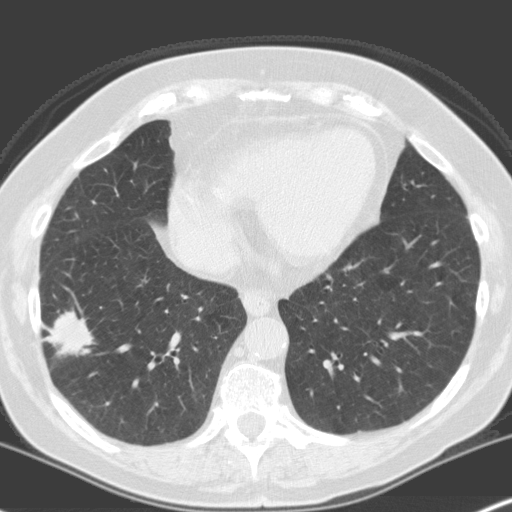
Low-dose screening chest CT, one axial slice. Position 64 of 160 along the scan axis. 120 kVp. Lung window (W 1500 / L -600 HU). 3.2 mm slice thickness. 512 × 512 image matrix, field of view 316 × 316 mm.
Structures marked on this image (outlined manually by an expert reader):
- lesion 1 (tumor, lower lobe of right lung): bounding box <45,311,93,357> (left, top, right, bottom; pixels)